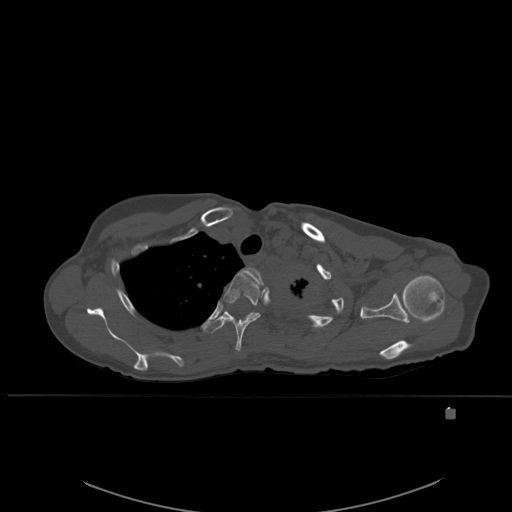
CT including the spine, one axial slice; bone window (W 1800 / L 400 HU); 512 × 512 image matrix. Female patient, age 45 years. From the clinical record (not read from this slice): primary cancer: lung.
Outlined on this slice (semi-automatically segmented with operator editing):
- T2 vertebra: bounding box (x1, y1, x2, y2) in pixels: (242, 268, 264, 291)
- T3 vertebra: (223, 271, 261, 352)
- T4 vertebra: (203, 305, 254, 333)